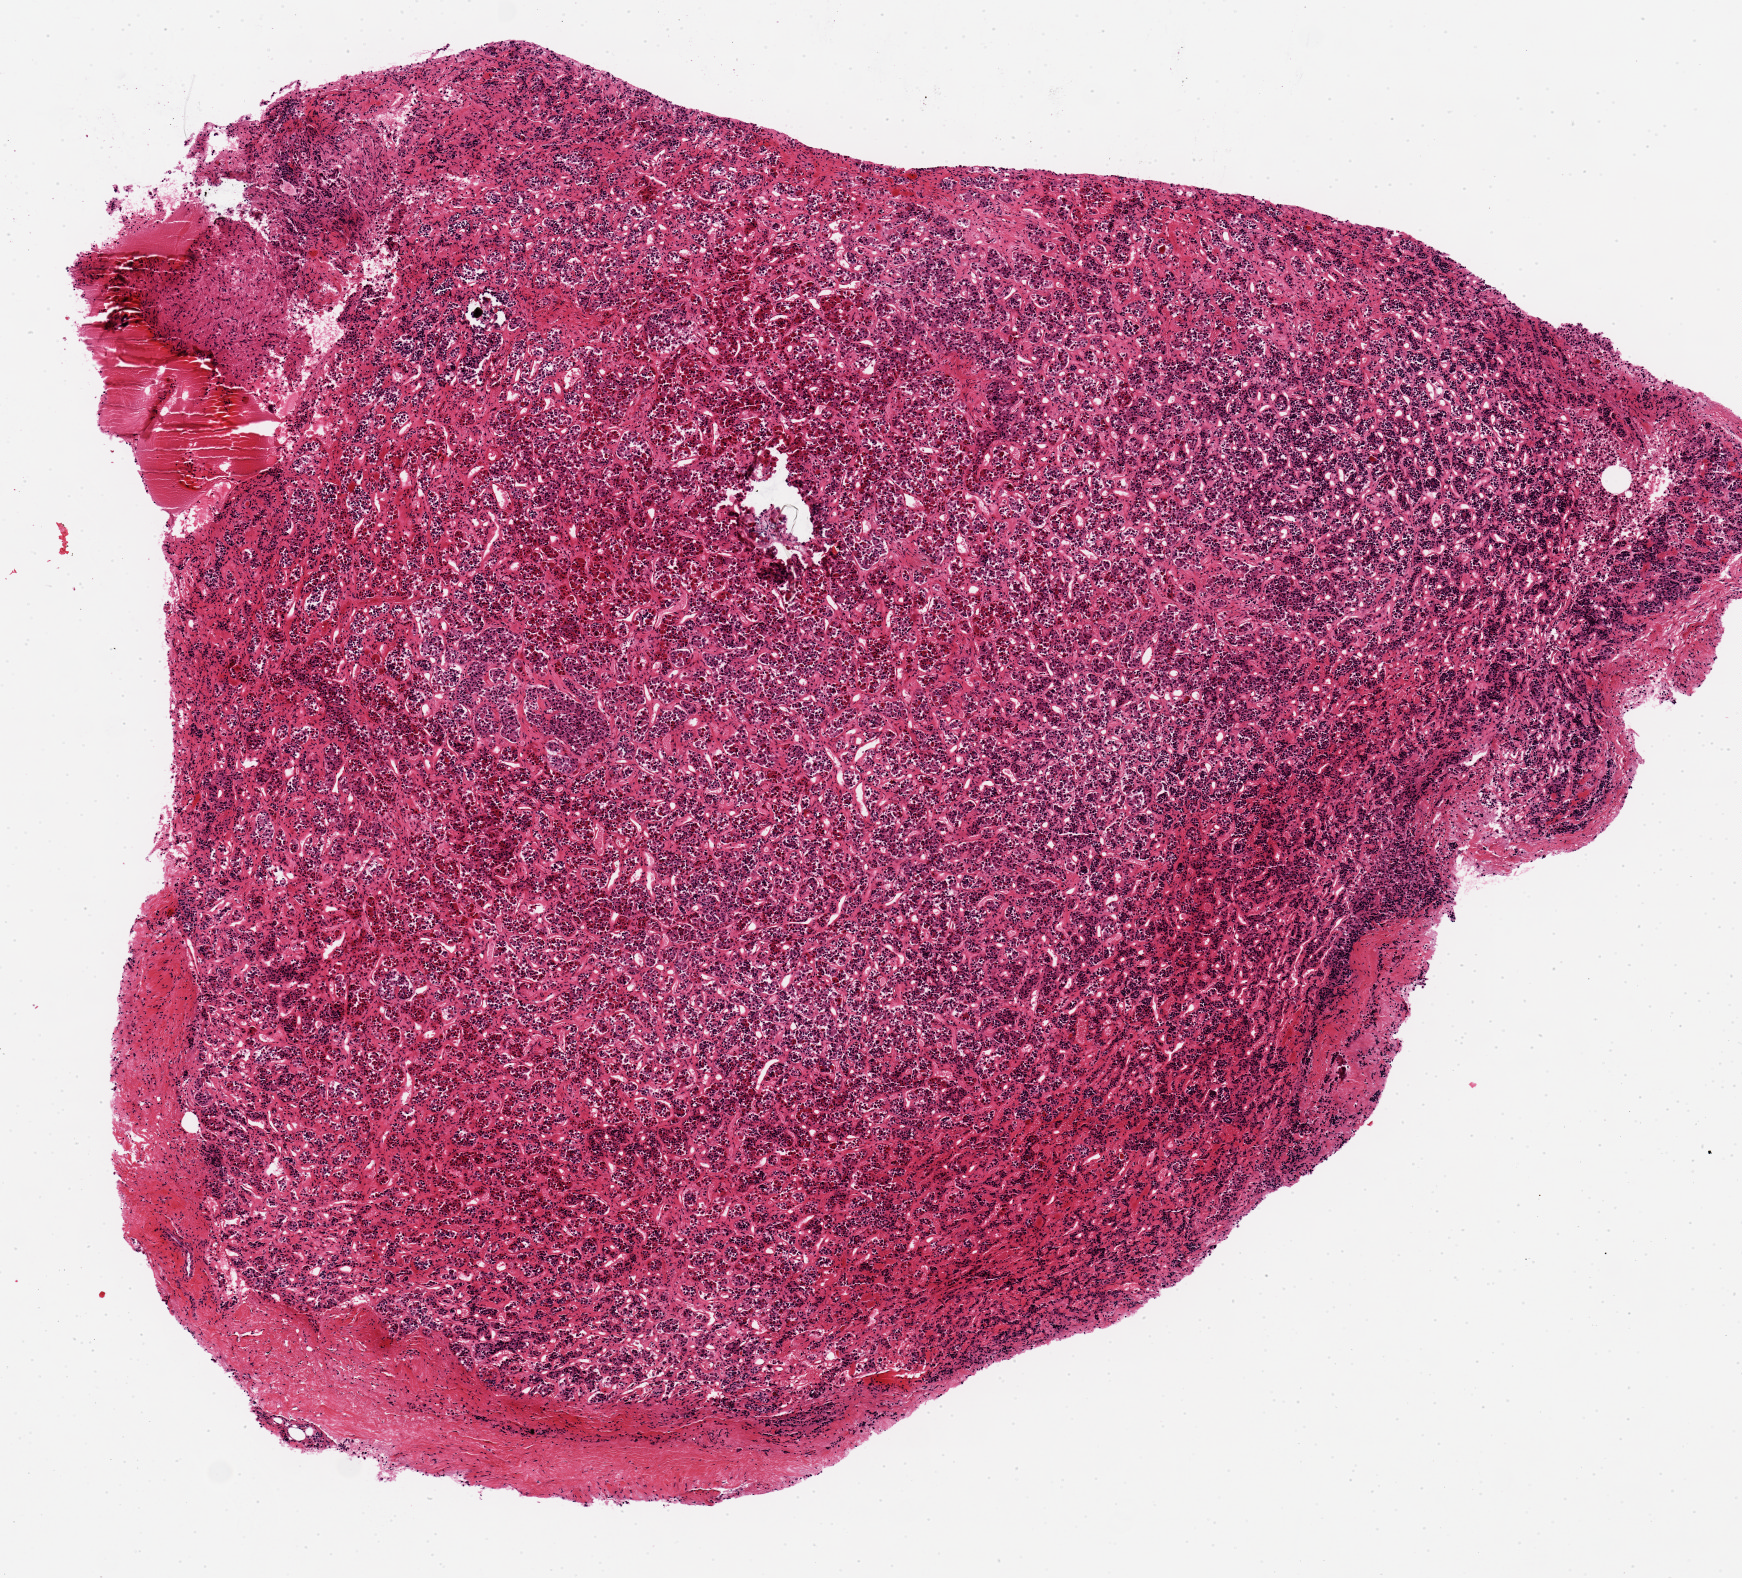
H&E whole-slide image, low-resolution overview of the scanned area, about 6.9 x 6.2 mm; PAXgene-fixed paraffin-embedded (PFPE) section; sampled site (target tissue): pituitary; donor tissue sample. Male donor.
• reviewer comment on this tissue sample: Anterior pituitary. 6.5x5.7mm